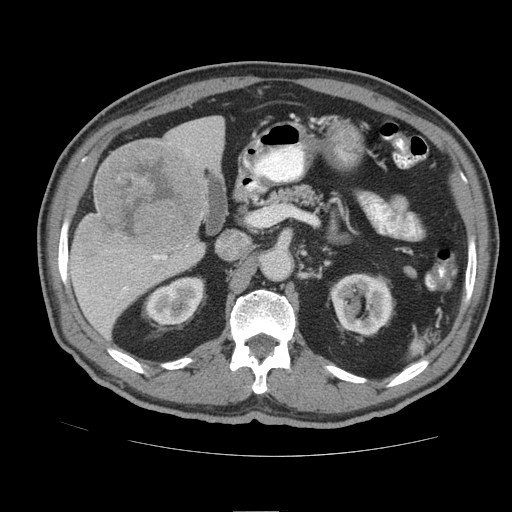
Contrast-enhanced abdominal CT (liver protocol), one axial slice. Position 46 of 105 along the scan axis. Reconstruction kernel STANDARD. Soft-tissue window (W 400 / L 40 HU). 2.5 mm slice thickness. 512 × 512 image matrix, field of view 380 × 380 mm. Case-level facts recorded for this patient, not image findings: diagnosis: hepatocellular carcinoma (patient treated with transarterial chemoembolisation; whether this scan precedes or follows treatment is not stated here); TNM stage (as recorded): Stage-IIIB; Child-Pugh class: A; tumour nodularity: multinodular.
Structures marked on this image (semi-automatically segmented with operator editing):
- liver parenchyma outside the tumour (the mass and vessels are separate outlines, so this box may not span the whole liver): bounding box [x1, y1, x2, y2] px = [68, 116, 224, 338]
- mass: [83, 141, 202, 252]
- liver vessels: [85, 255, 167, 292]